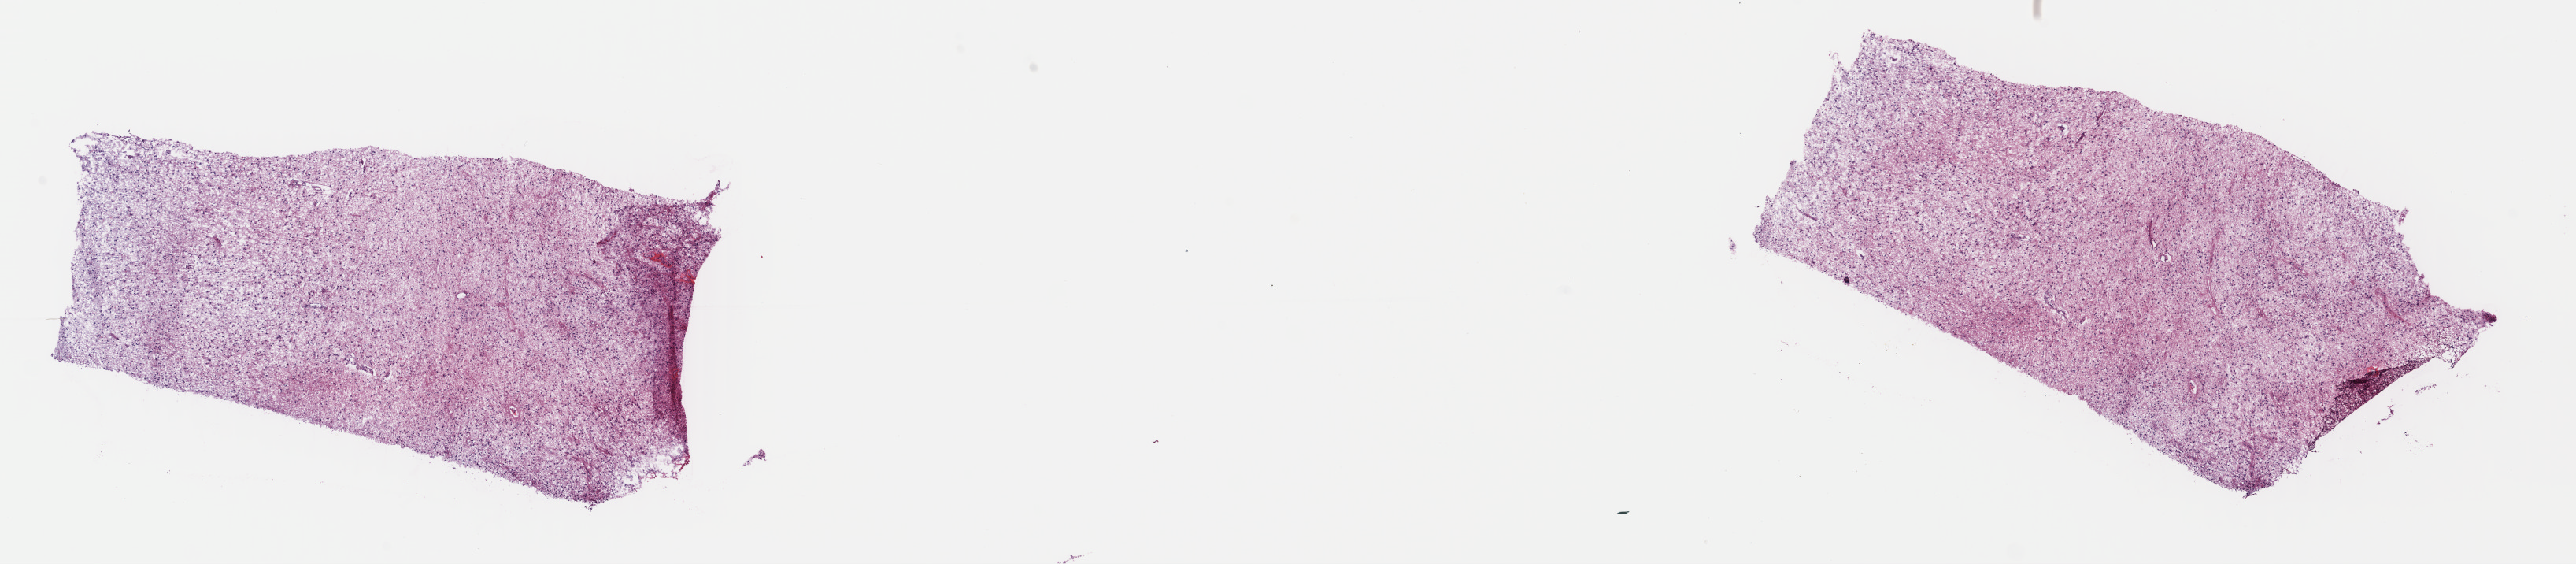
Whole-slide histology image, H&E, shown as a low-resolution overview of the whole scanned area (about 25.7 x 5.6 mm, from a 40x scan), frozen section, brain, primary tumour sample. Male, age 47 years at initial diagnosis. Histologic grade: G2 (moderately differentiated). Pathologist review of this section (percent, as recorded): tumour cells 50%, tumour nuclei 80%, normal cells 5%, stromal cells 45%, necrosis 0%. Inflammatory infiltration, as recorded: lymphocyte infiltration 0%, monocyte infiltration 0%, neutrophil infiltration 0%.
- laterality: right
- diagnosis: Astrocytoma, NOS